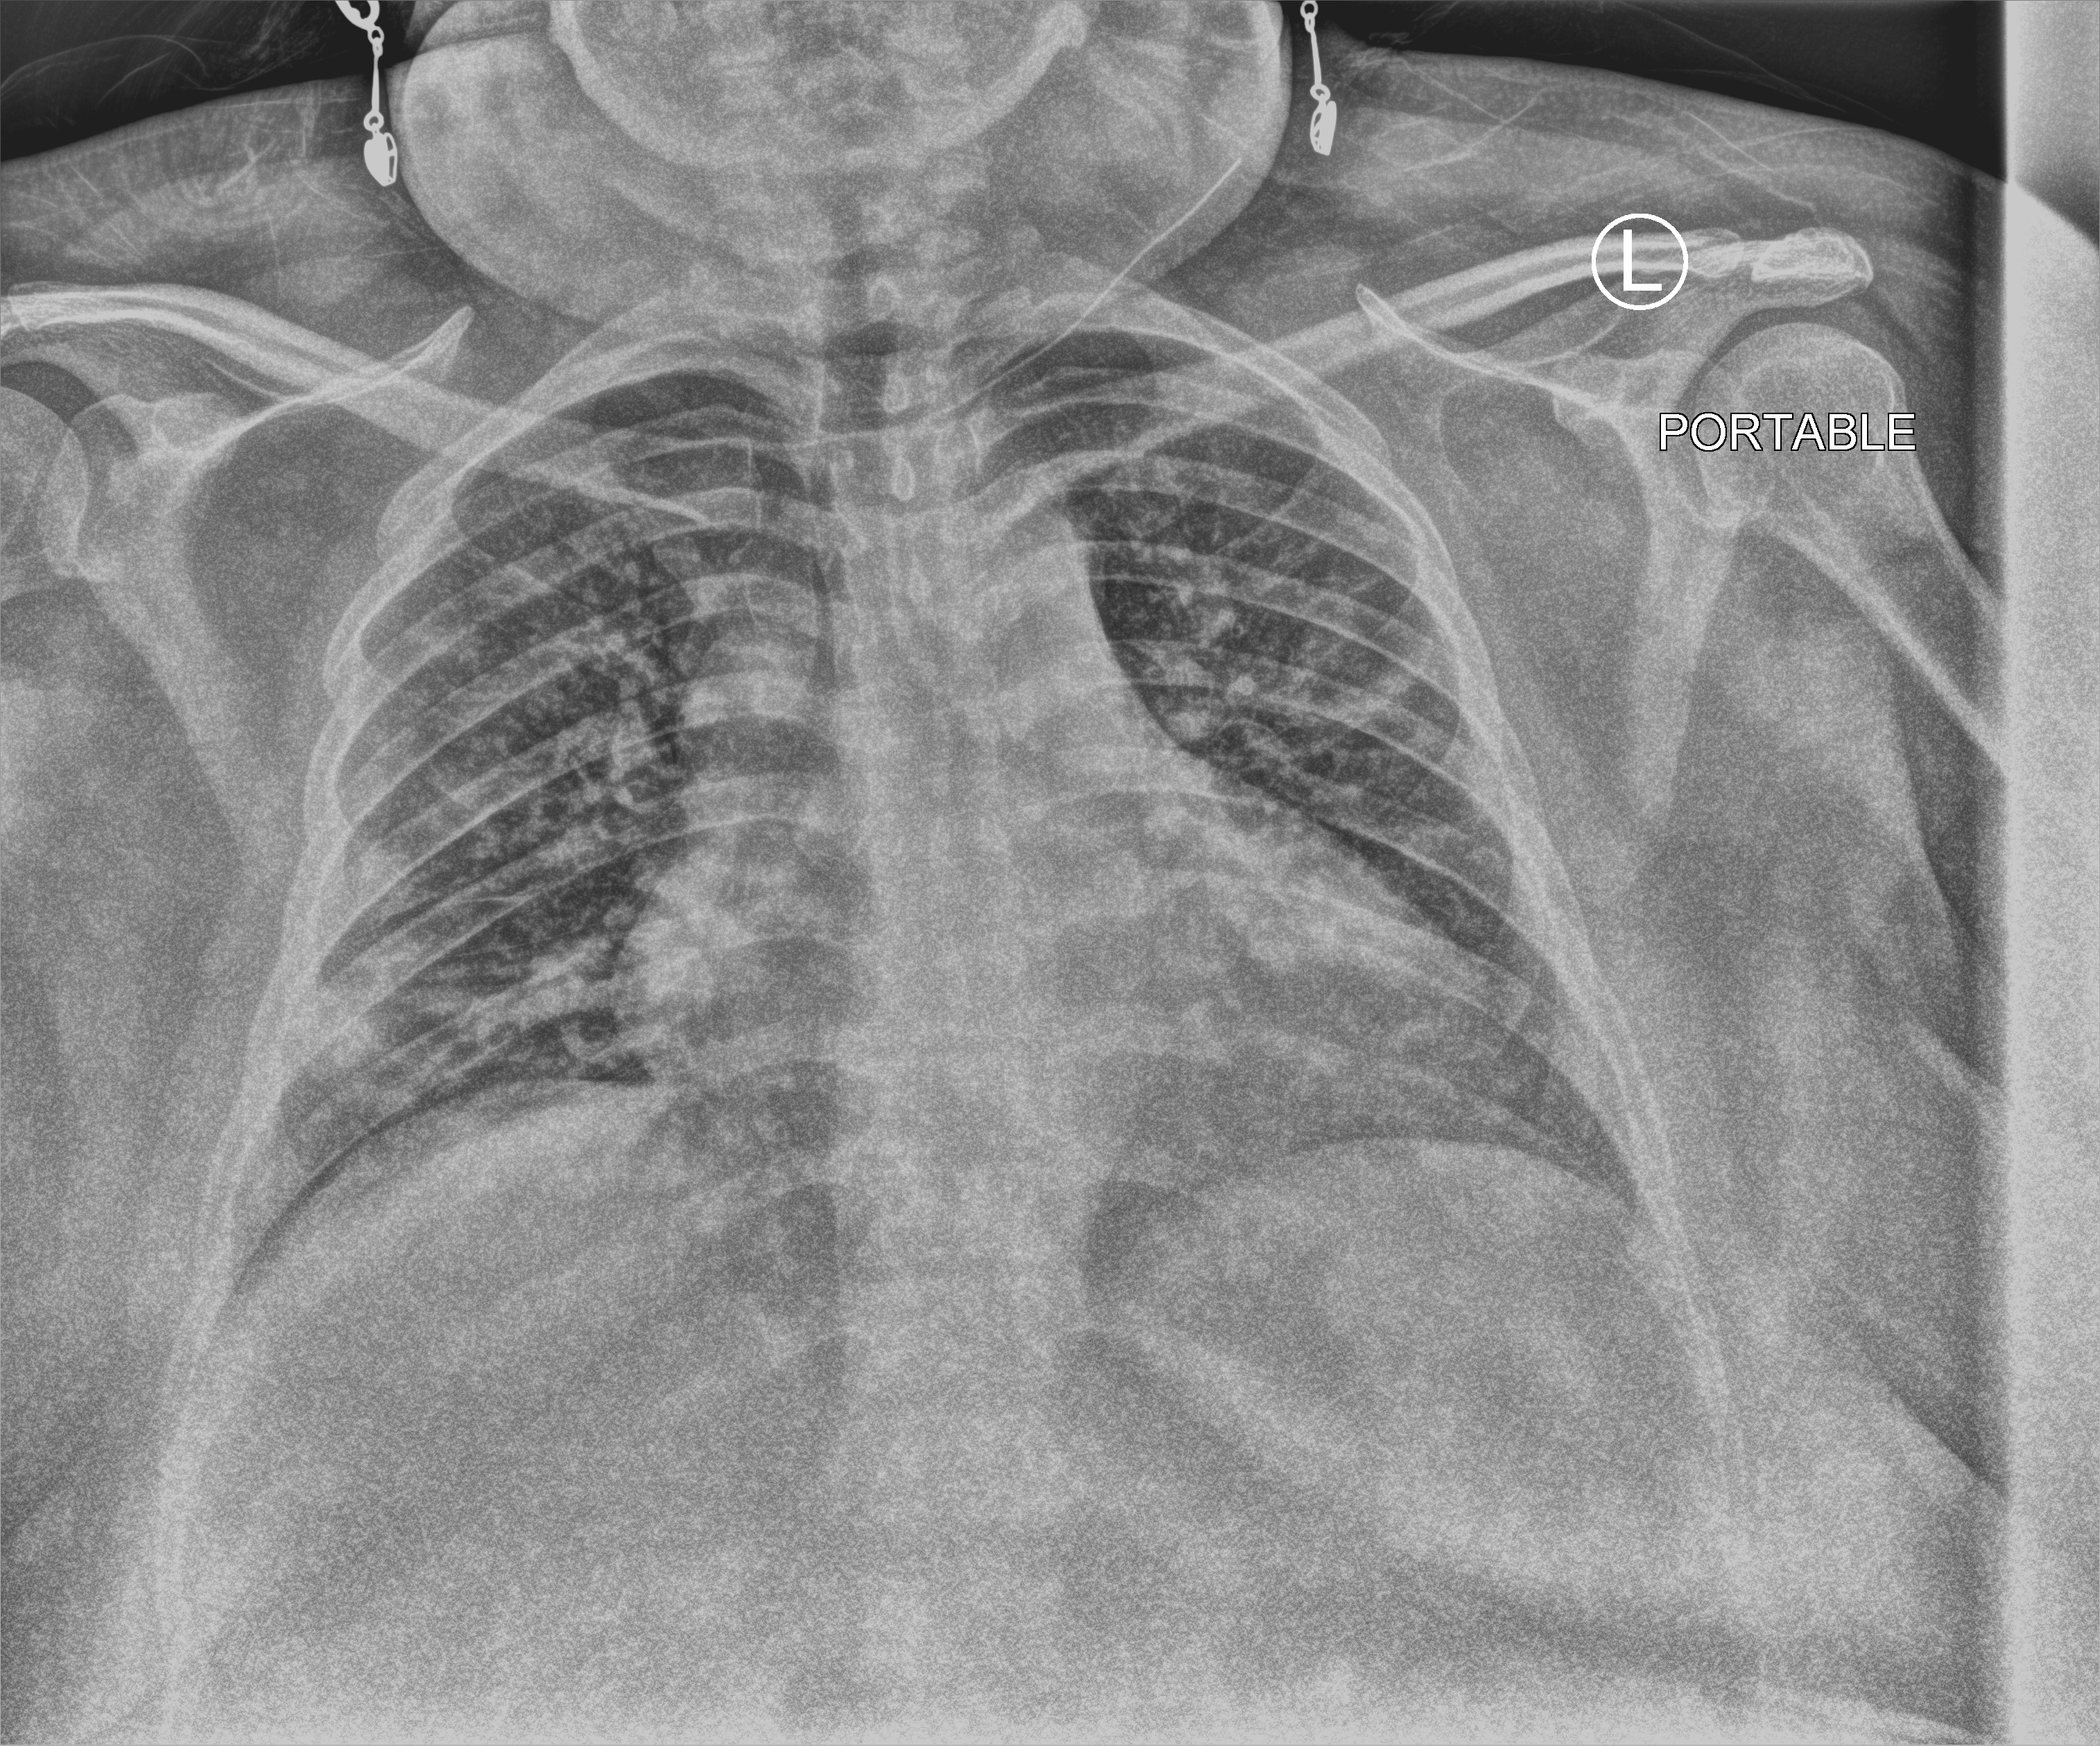
Chest X-ray (portable), anteroposterior (AP) projection. Female patient hospitalised with COVID-19, age 18–59 years.
From the hospital-stay record, not from the radiograph (when in the stay this image was taken is not recorded): mechanically ventilated during this hospital stay: yes; chronic kidney disease (admission record): no.